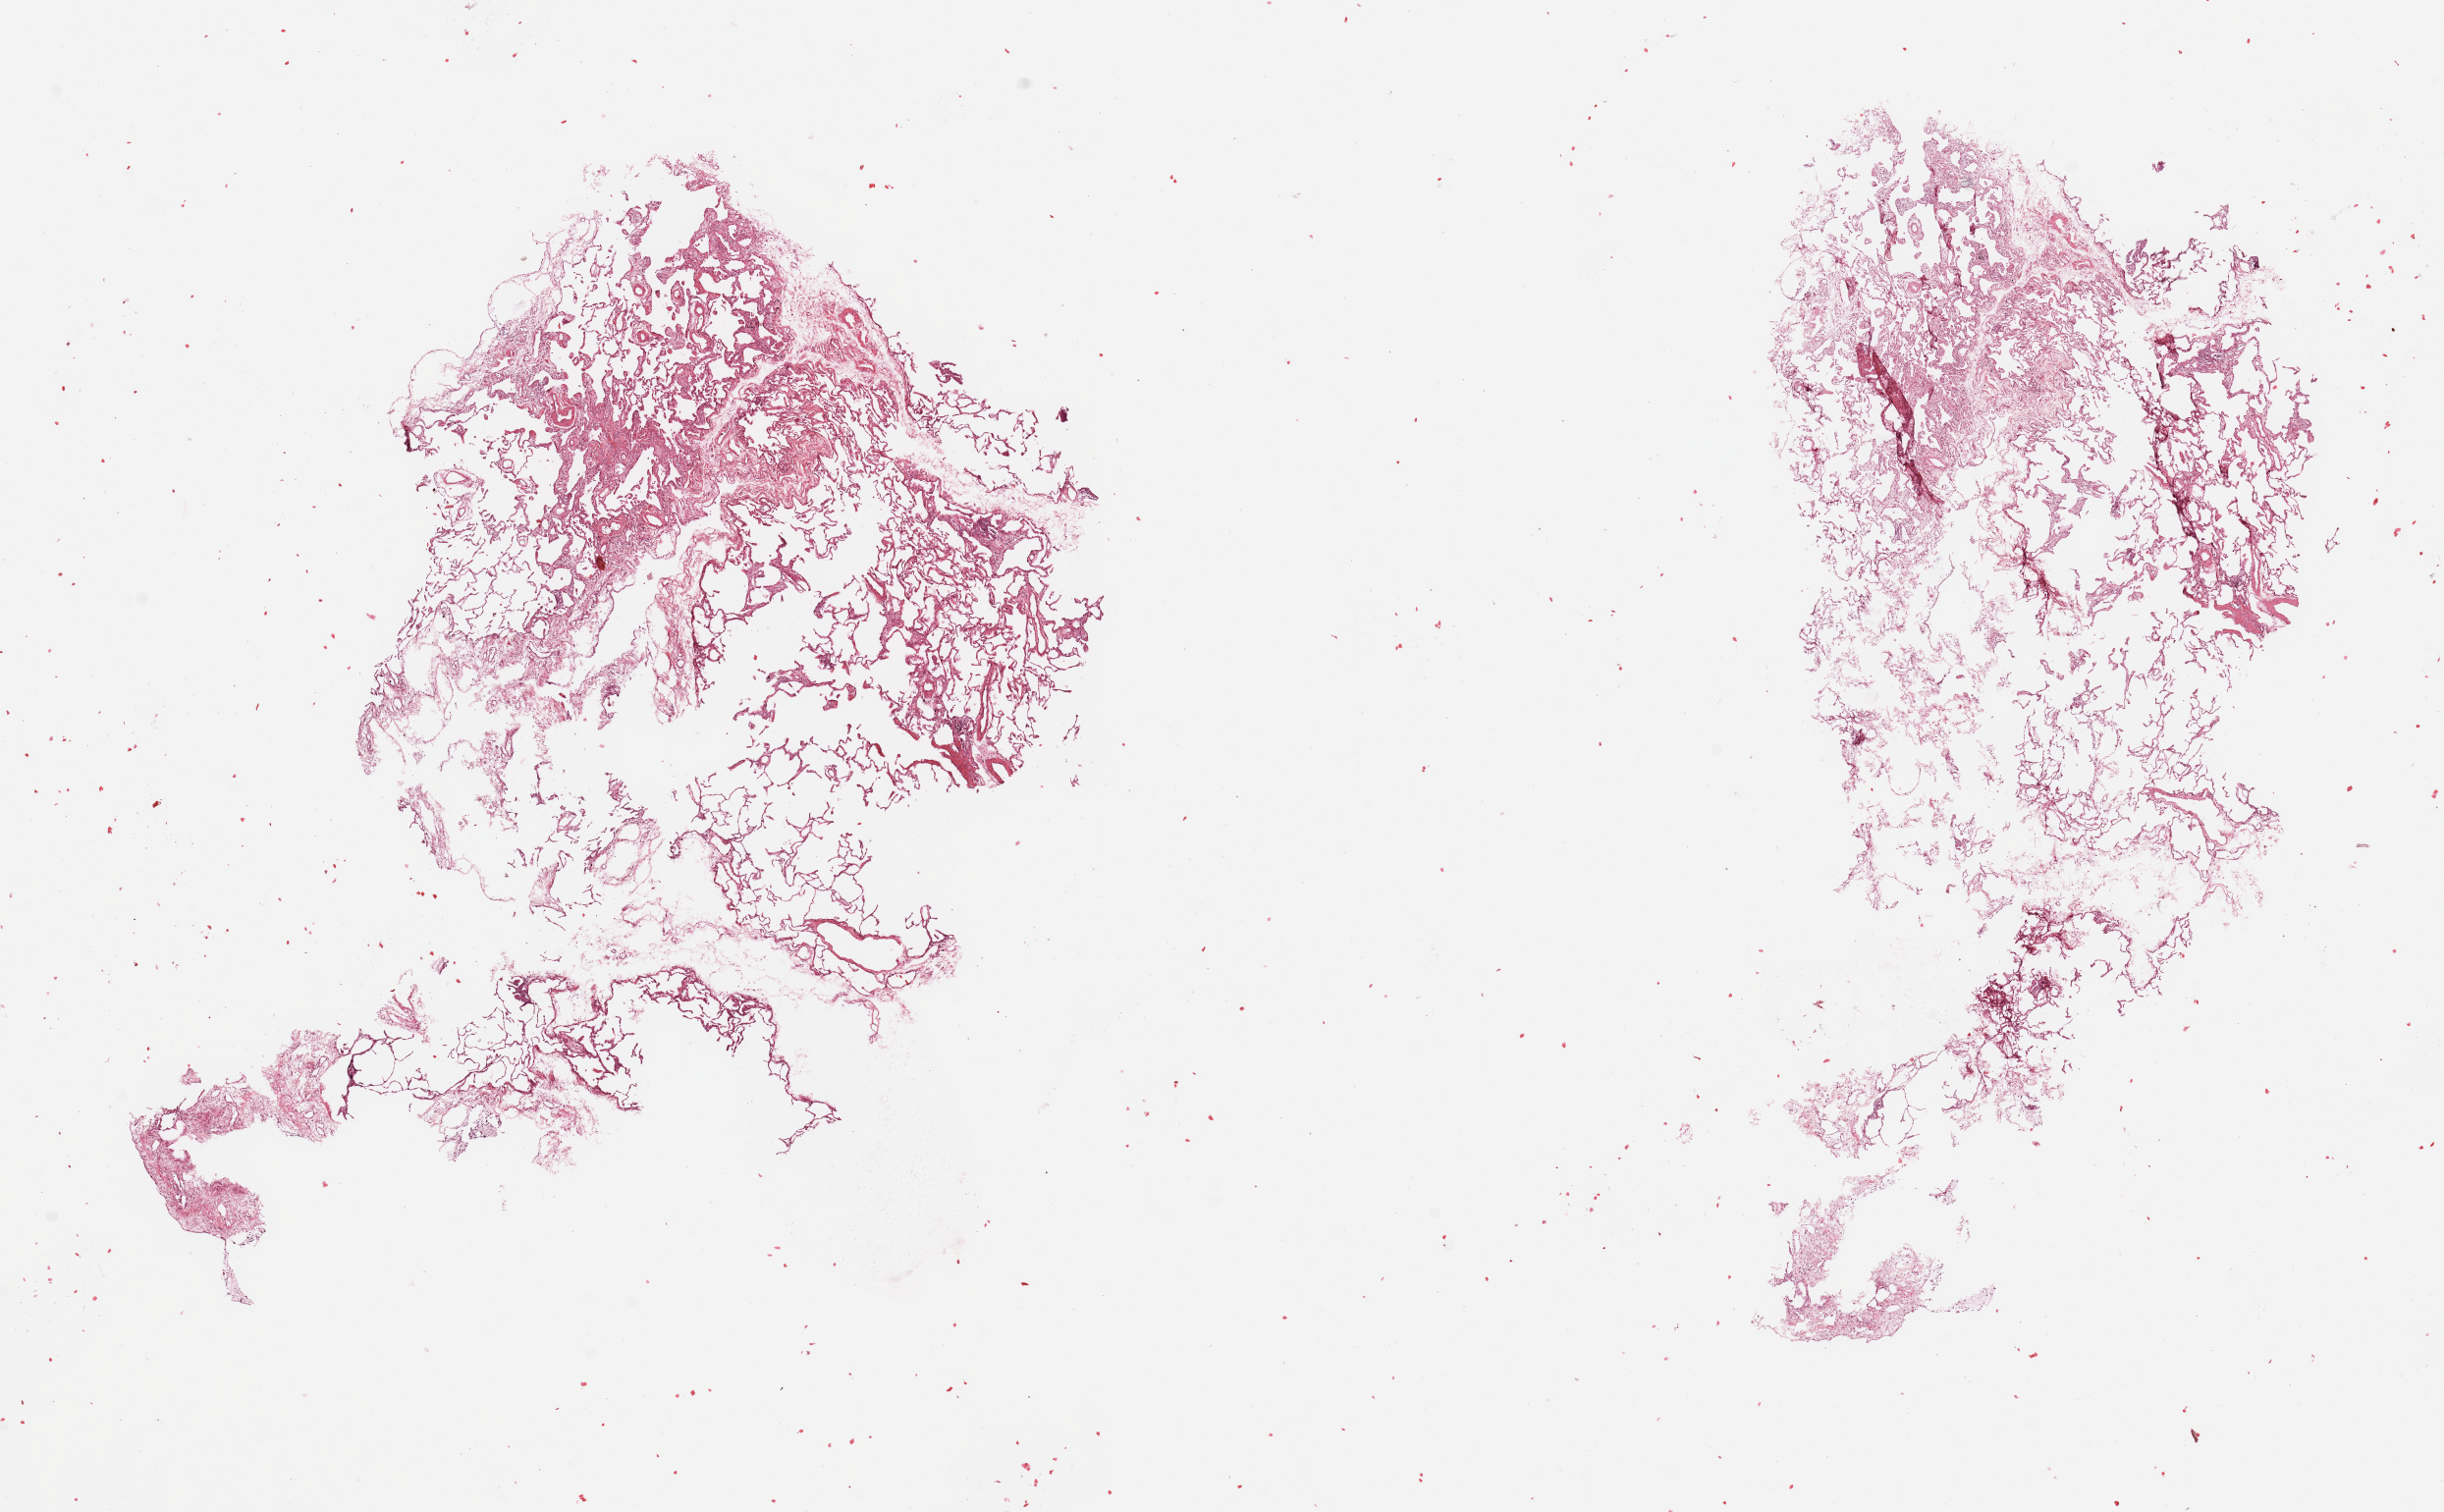
Whole-slide histology image, Hematoxylin and eosin (H&E) stained — whole scanned area (about 19.7 x 12.2 mm) shown as a low-resolution overview. Normal (non-tumour) tissue sample, sampled site: lung. 64-year-old female patient.
* this section: normal (non-tumour) tissue from the same patient
* patient diagnosis: Squamous cell carcinoma, NOS